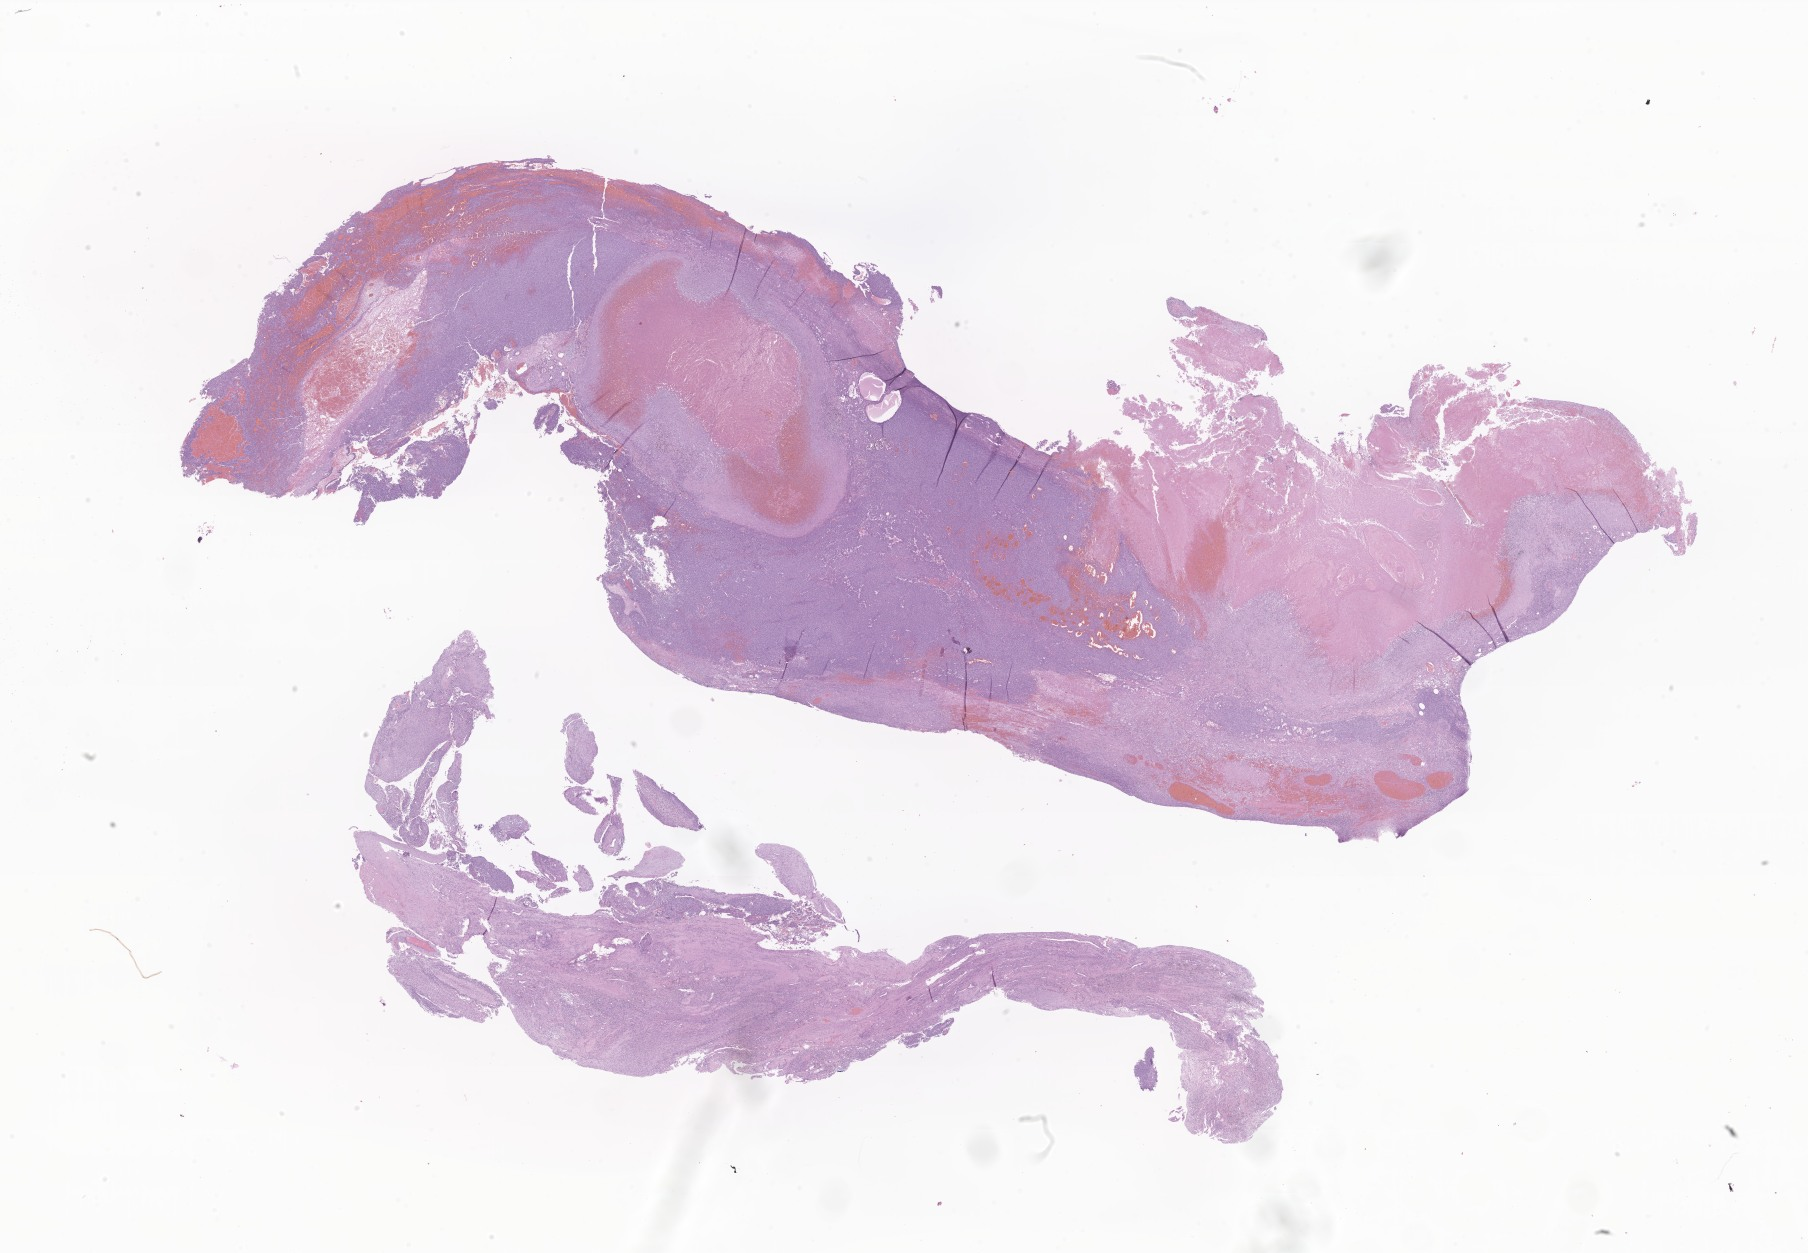
Whole-slide image, hematoxylin and eosin (H&E) stain of tumor tissue from the soft tissue of trunk — shown as a low-resolution overview of the whole scanned area (about 30.5 x 21.1 mm). FFPE section. Male patient, age 220 months (18 years 4 months).
Tissue or organ of origin (case record): connective, subcutaneous and other soft tissues of trunk. Recorded diagnosis: Ewing sarcoma.